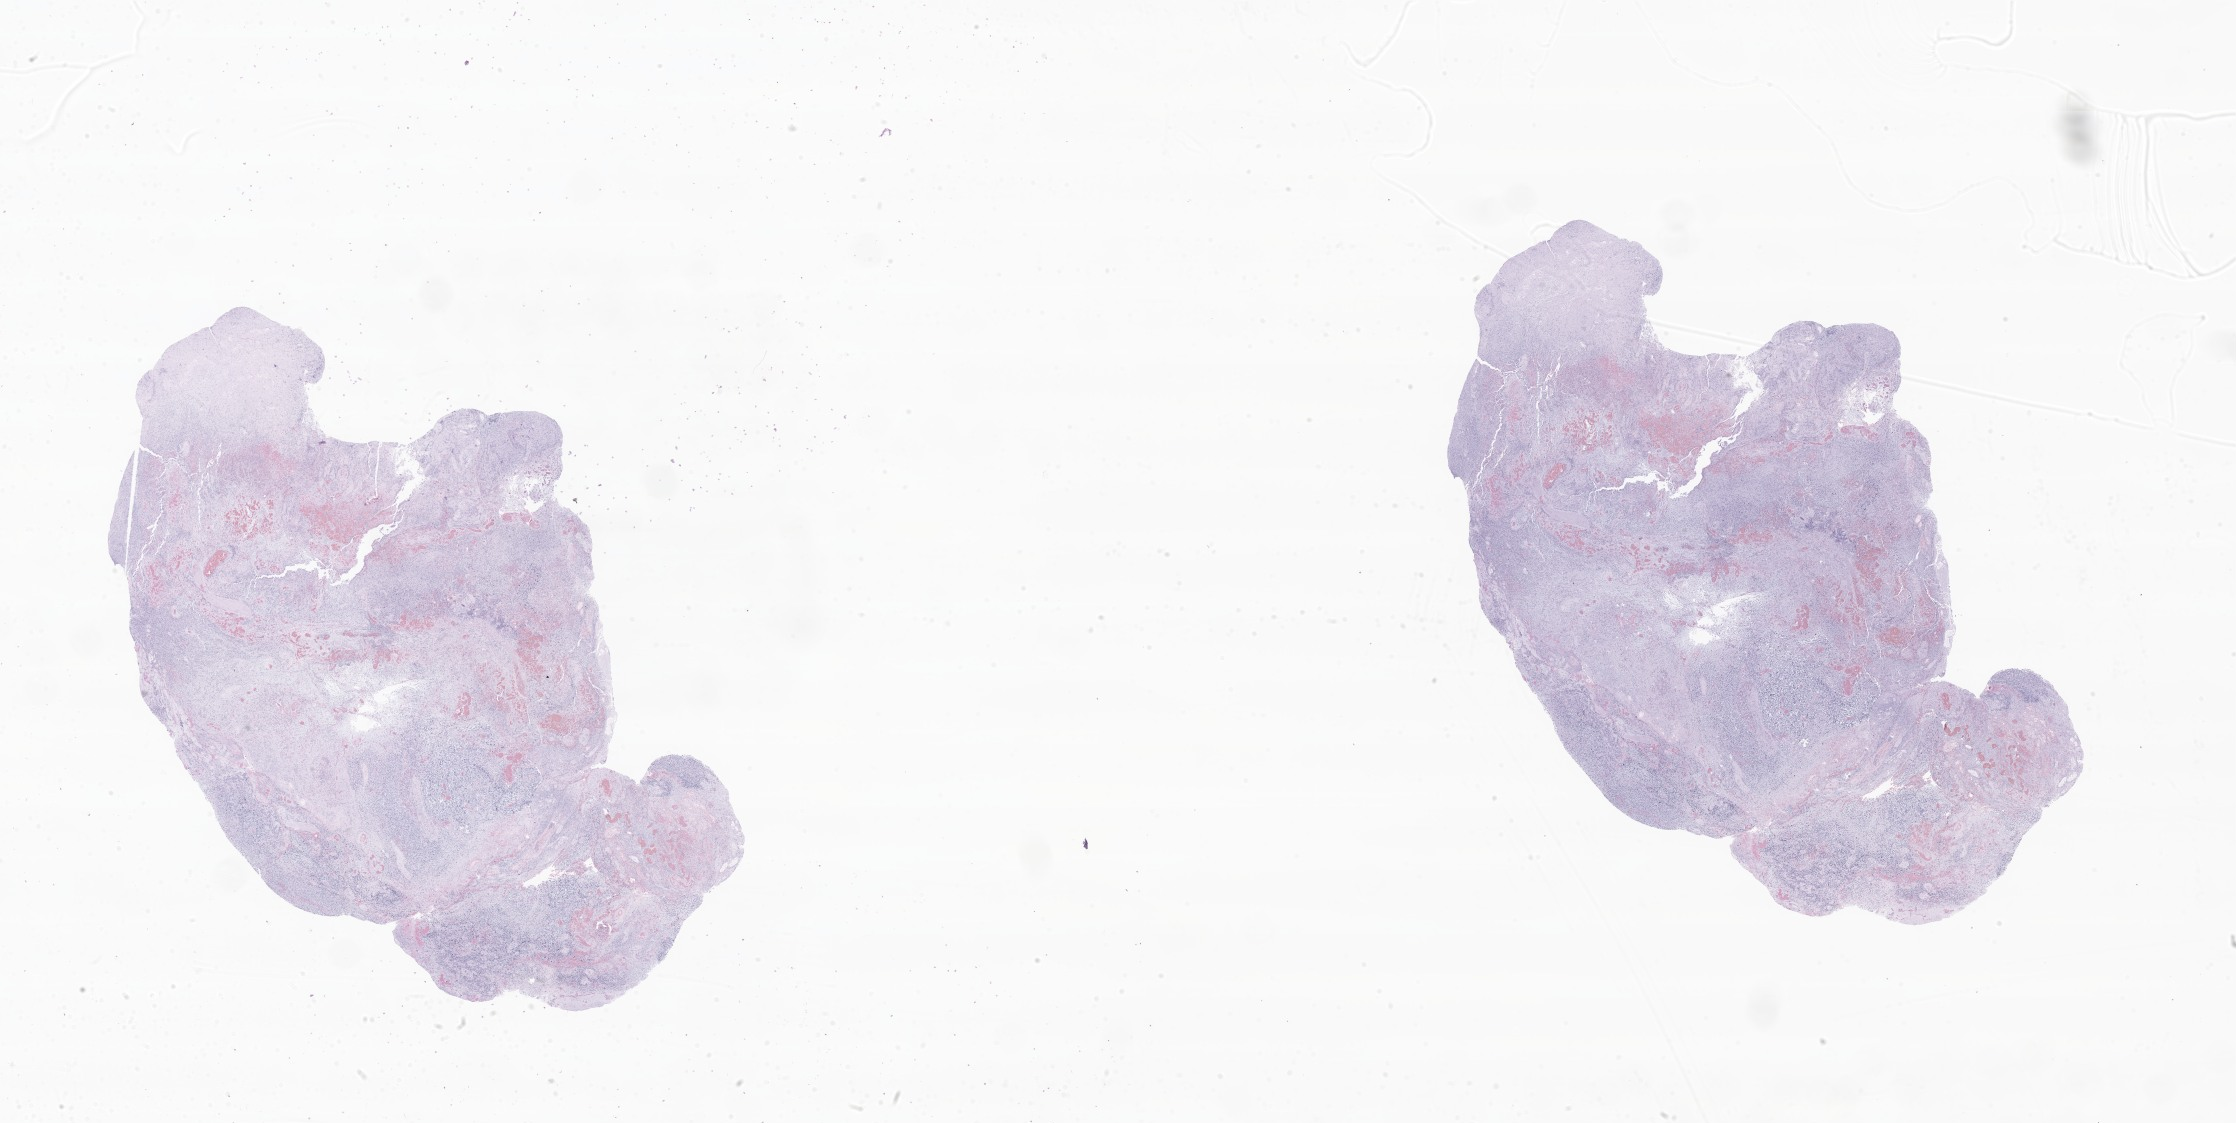
Whole-slide image, hematoxylin and eosin (H&E) stain of tumor tissue from the brain — whole scanned area (about 37.7 x 18.9 mm) shown as a low-resolution overview, formalin-fixed, paraffin-embedded (FFPE) tissue. Patient male; age 169 months (14 years 1 month).
Diagnosis: Neoplasm, uncertain whether benign or malignant.